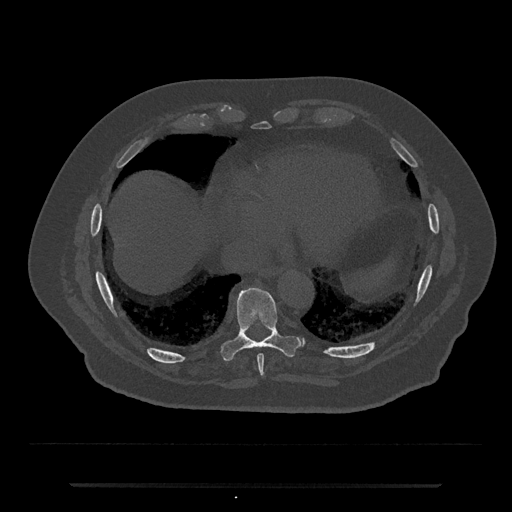
CT including the spine, one axial slice. Position 764 of 797 along the scan axis. Reconstruction kernel Br40s/3. Bone window (W 1800 / L 400 HU). 0.5 mm slice thickness. 512 × 512 image matrix. Male patient, age 80 years. Case-level facts recorded for this patient, not image findings: primary cancer: prostate; vertebrae with lytic lesions (as recorded): L1, T11.
Outlined on this slice (semi-automatic segmentation, software-assisted and operator-edited):
- T8 vertebra: box from (x=257, y=354) to (x=264, y=377) px
- T9 vertebra: (x=222, y=285)–(x=303, y=361)